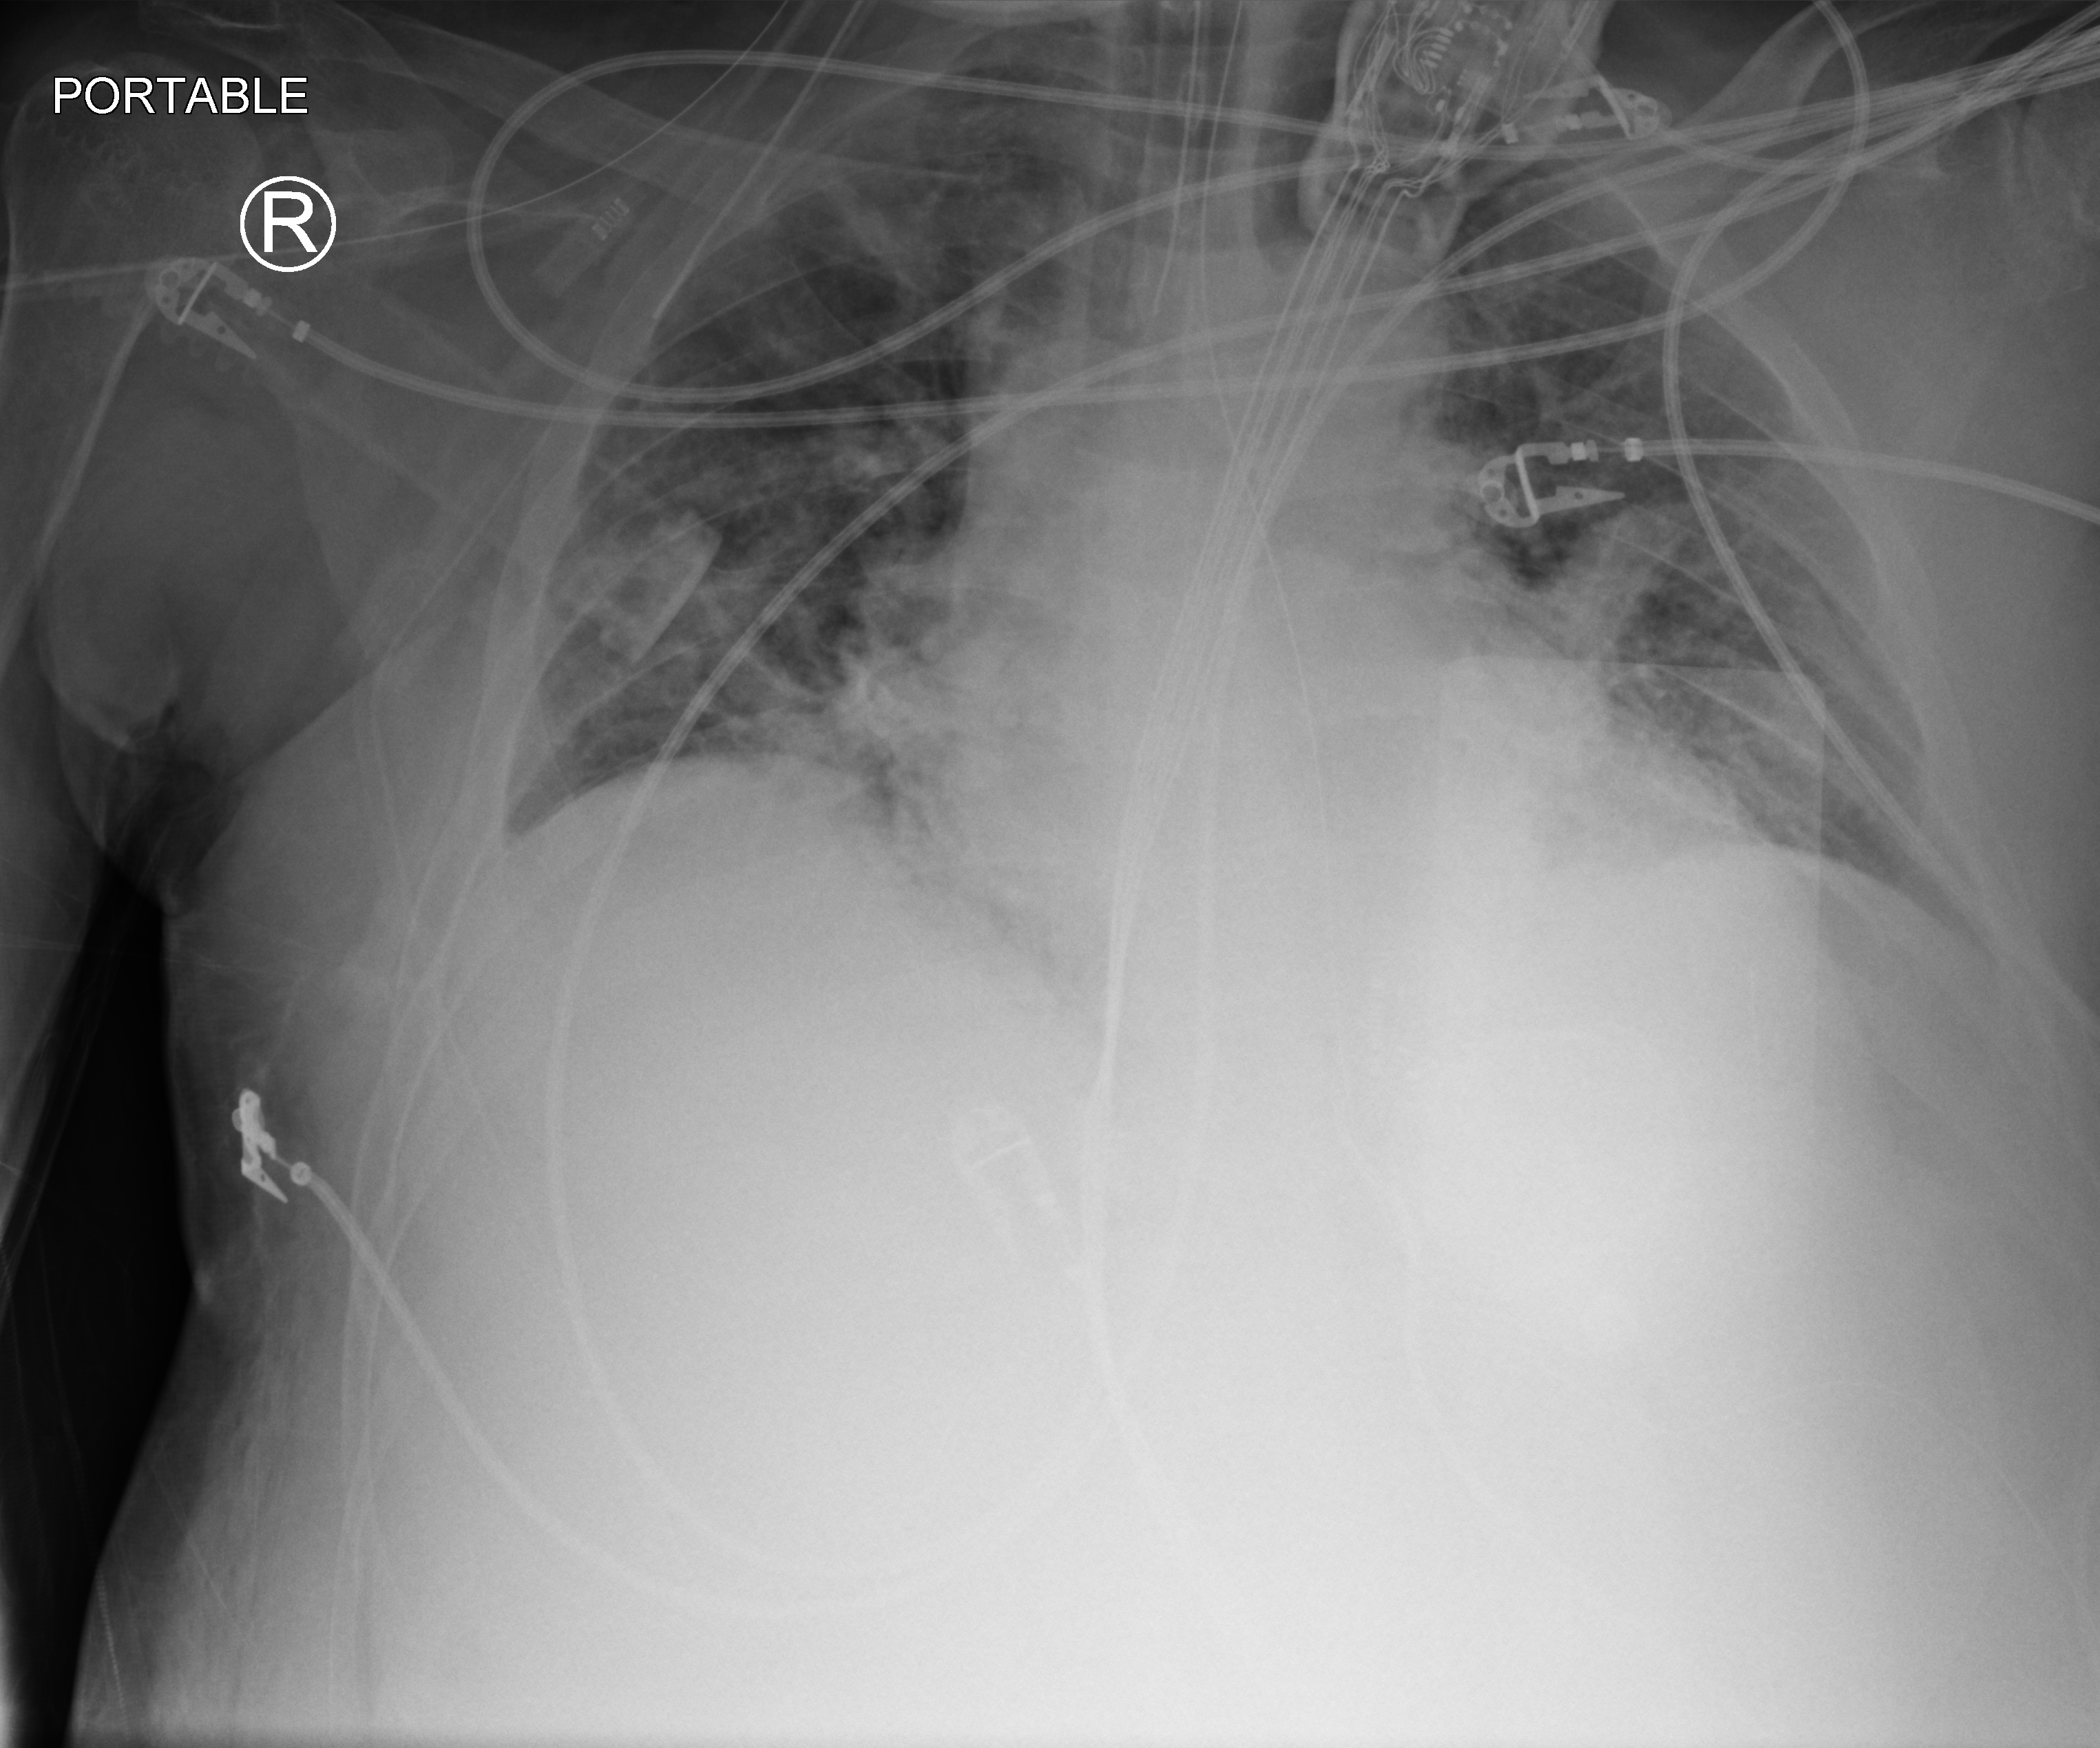
Portable chest radiograph. Patient hospitalised with COVID-19; male, aged 60–74 years.
Hospital-stay facts (about this admission, not read from this image; timing relative to this image not recorded): mechanically ventilated during this hospital stay: yes; COPD (admission record): no.